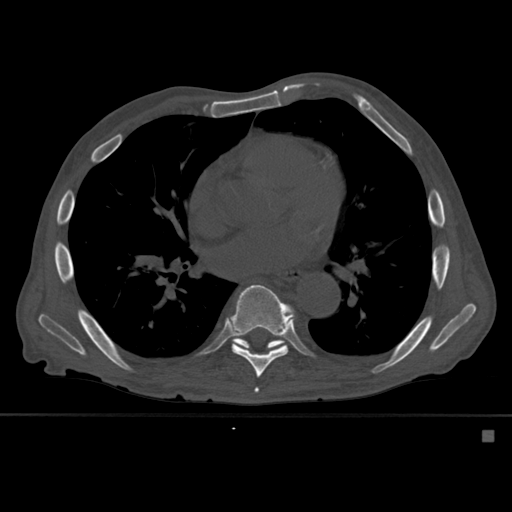
CT including the spine, one axial slice; slice 347 of 527 in the series (ordered by position); bone window (W 1800 / L 400 HU); 512 × 512 image matrix. Male patient, age 78 years. From the clinical record (not read from this slice): primary cancer: prostate.
Annotated regions visible in this slice (semi-automatic segmentation, software-assisted and operator-edited):
- T7 vertebra: bounding box [x1, y1, x2, y2] px = [254, 387, 259, 393]
- T8 vertebra: [226, 284, 296, 378]
- T9 vertebra: [231, 335, 286, 350]